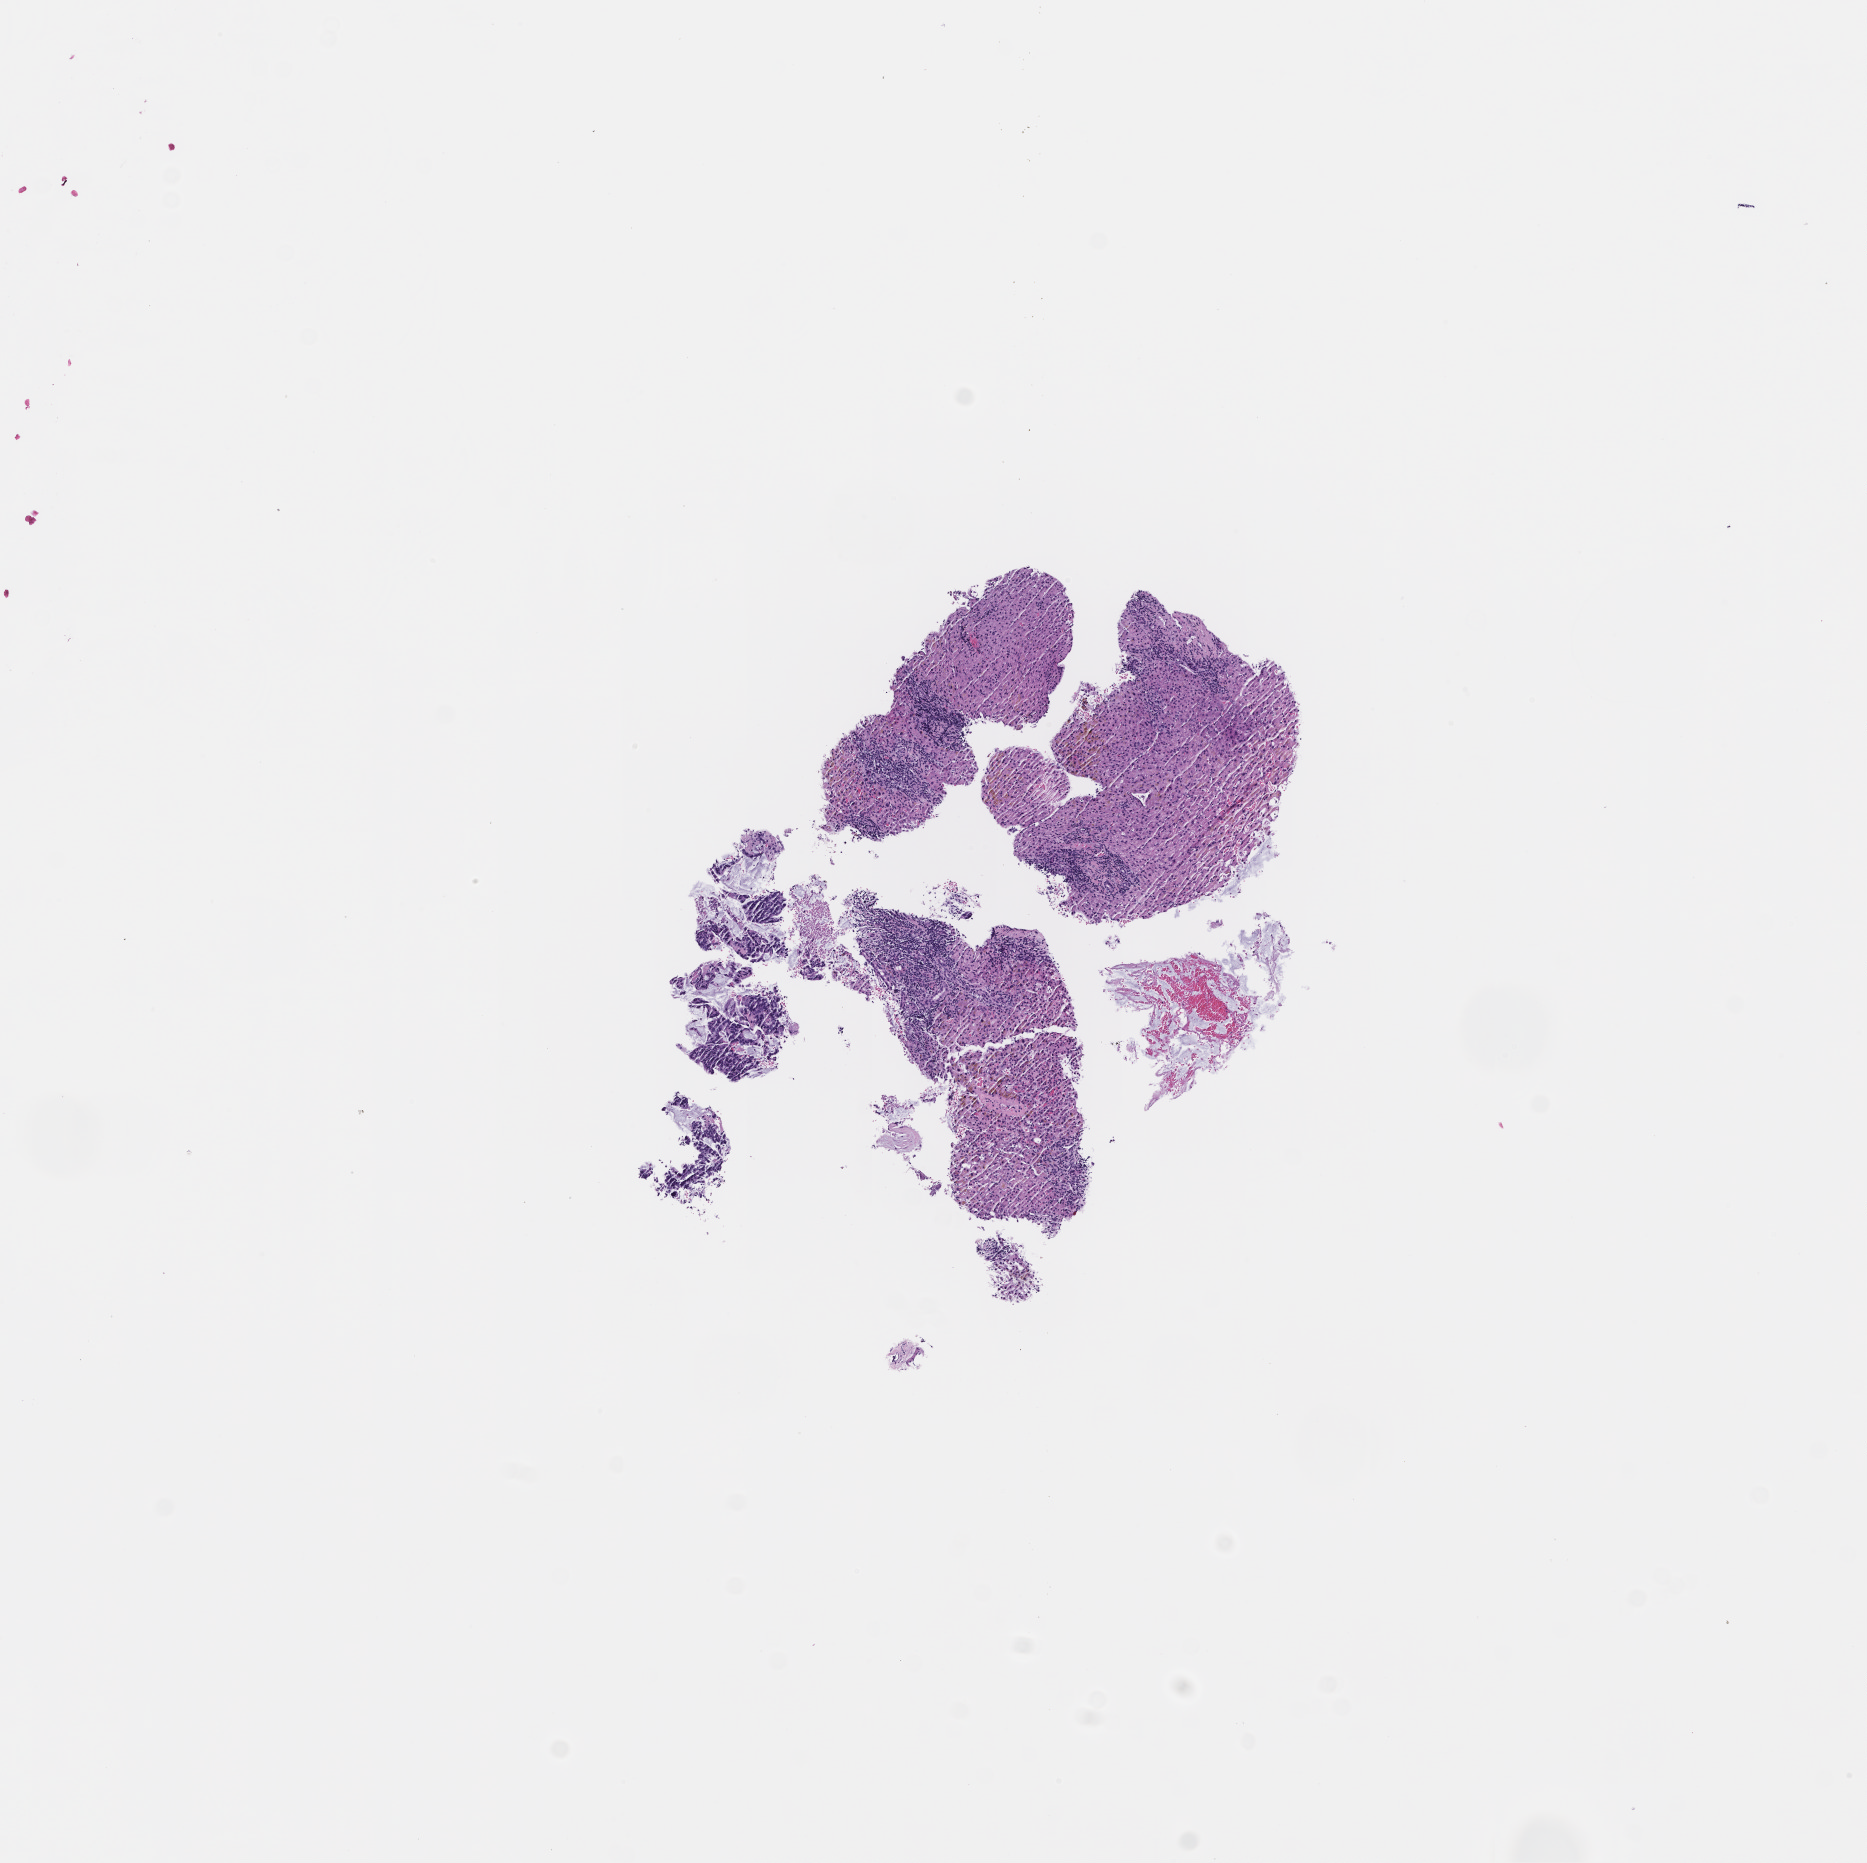
Whole-slide image, H&E stain — a low-resolution overview of the entire scanned area, about 7.5 x 7.5 mm. Formalin-fixed paraffin-embedded section. Female patient.
* this section: metastatic tumor tissue
* patient diagnosis (primary): Colorectal Carcinoma